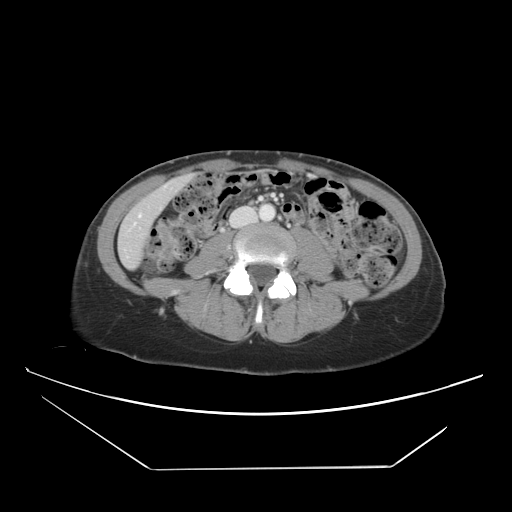
Contrast-enhanced abdominal CT, one axial slice; position 9 of 42 along the scan axis; intravenous contrast given; soft-tissue window (W 400 / L 40 HU); 5 mm slice thickness; 512 × 512 image matrix. Female patient, age 52 years. From the clinical record (not read from this slice): diagnosis: colorectal cancer liver metastases, imaged before liver resection; multiple liver metastases: yes.
Annotated regions visible in this slice (expert manual segmentation):
- hepatic veins: bounding box [x1, y1, x2, y2] px = [128, 184, 169, 232]
- liver: [120, 178, 187, 267]
- planned liver remnant (the part of the liver to remain after resection): [130, 177, 188, 222]
- portal vein (with intrahepatic branches): [259, 197, 263, 200]